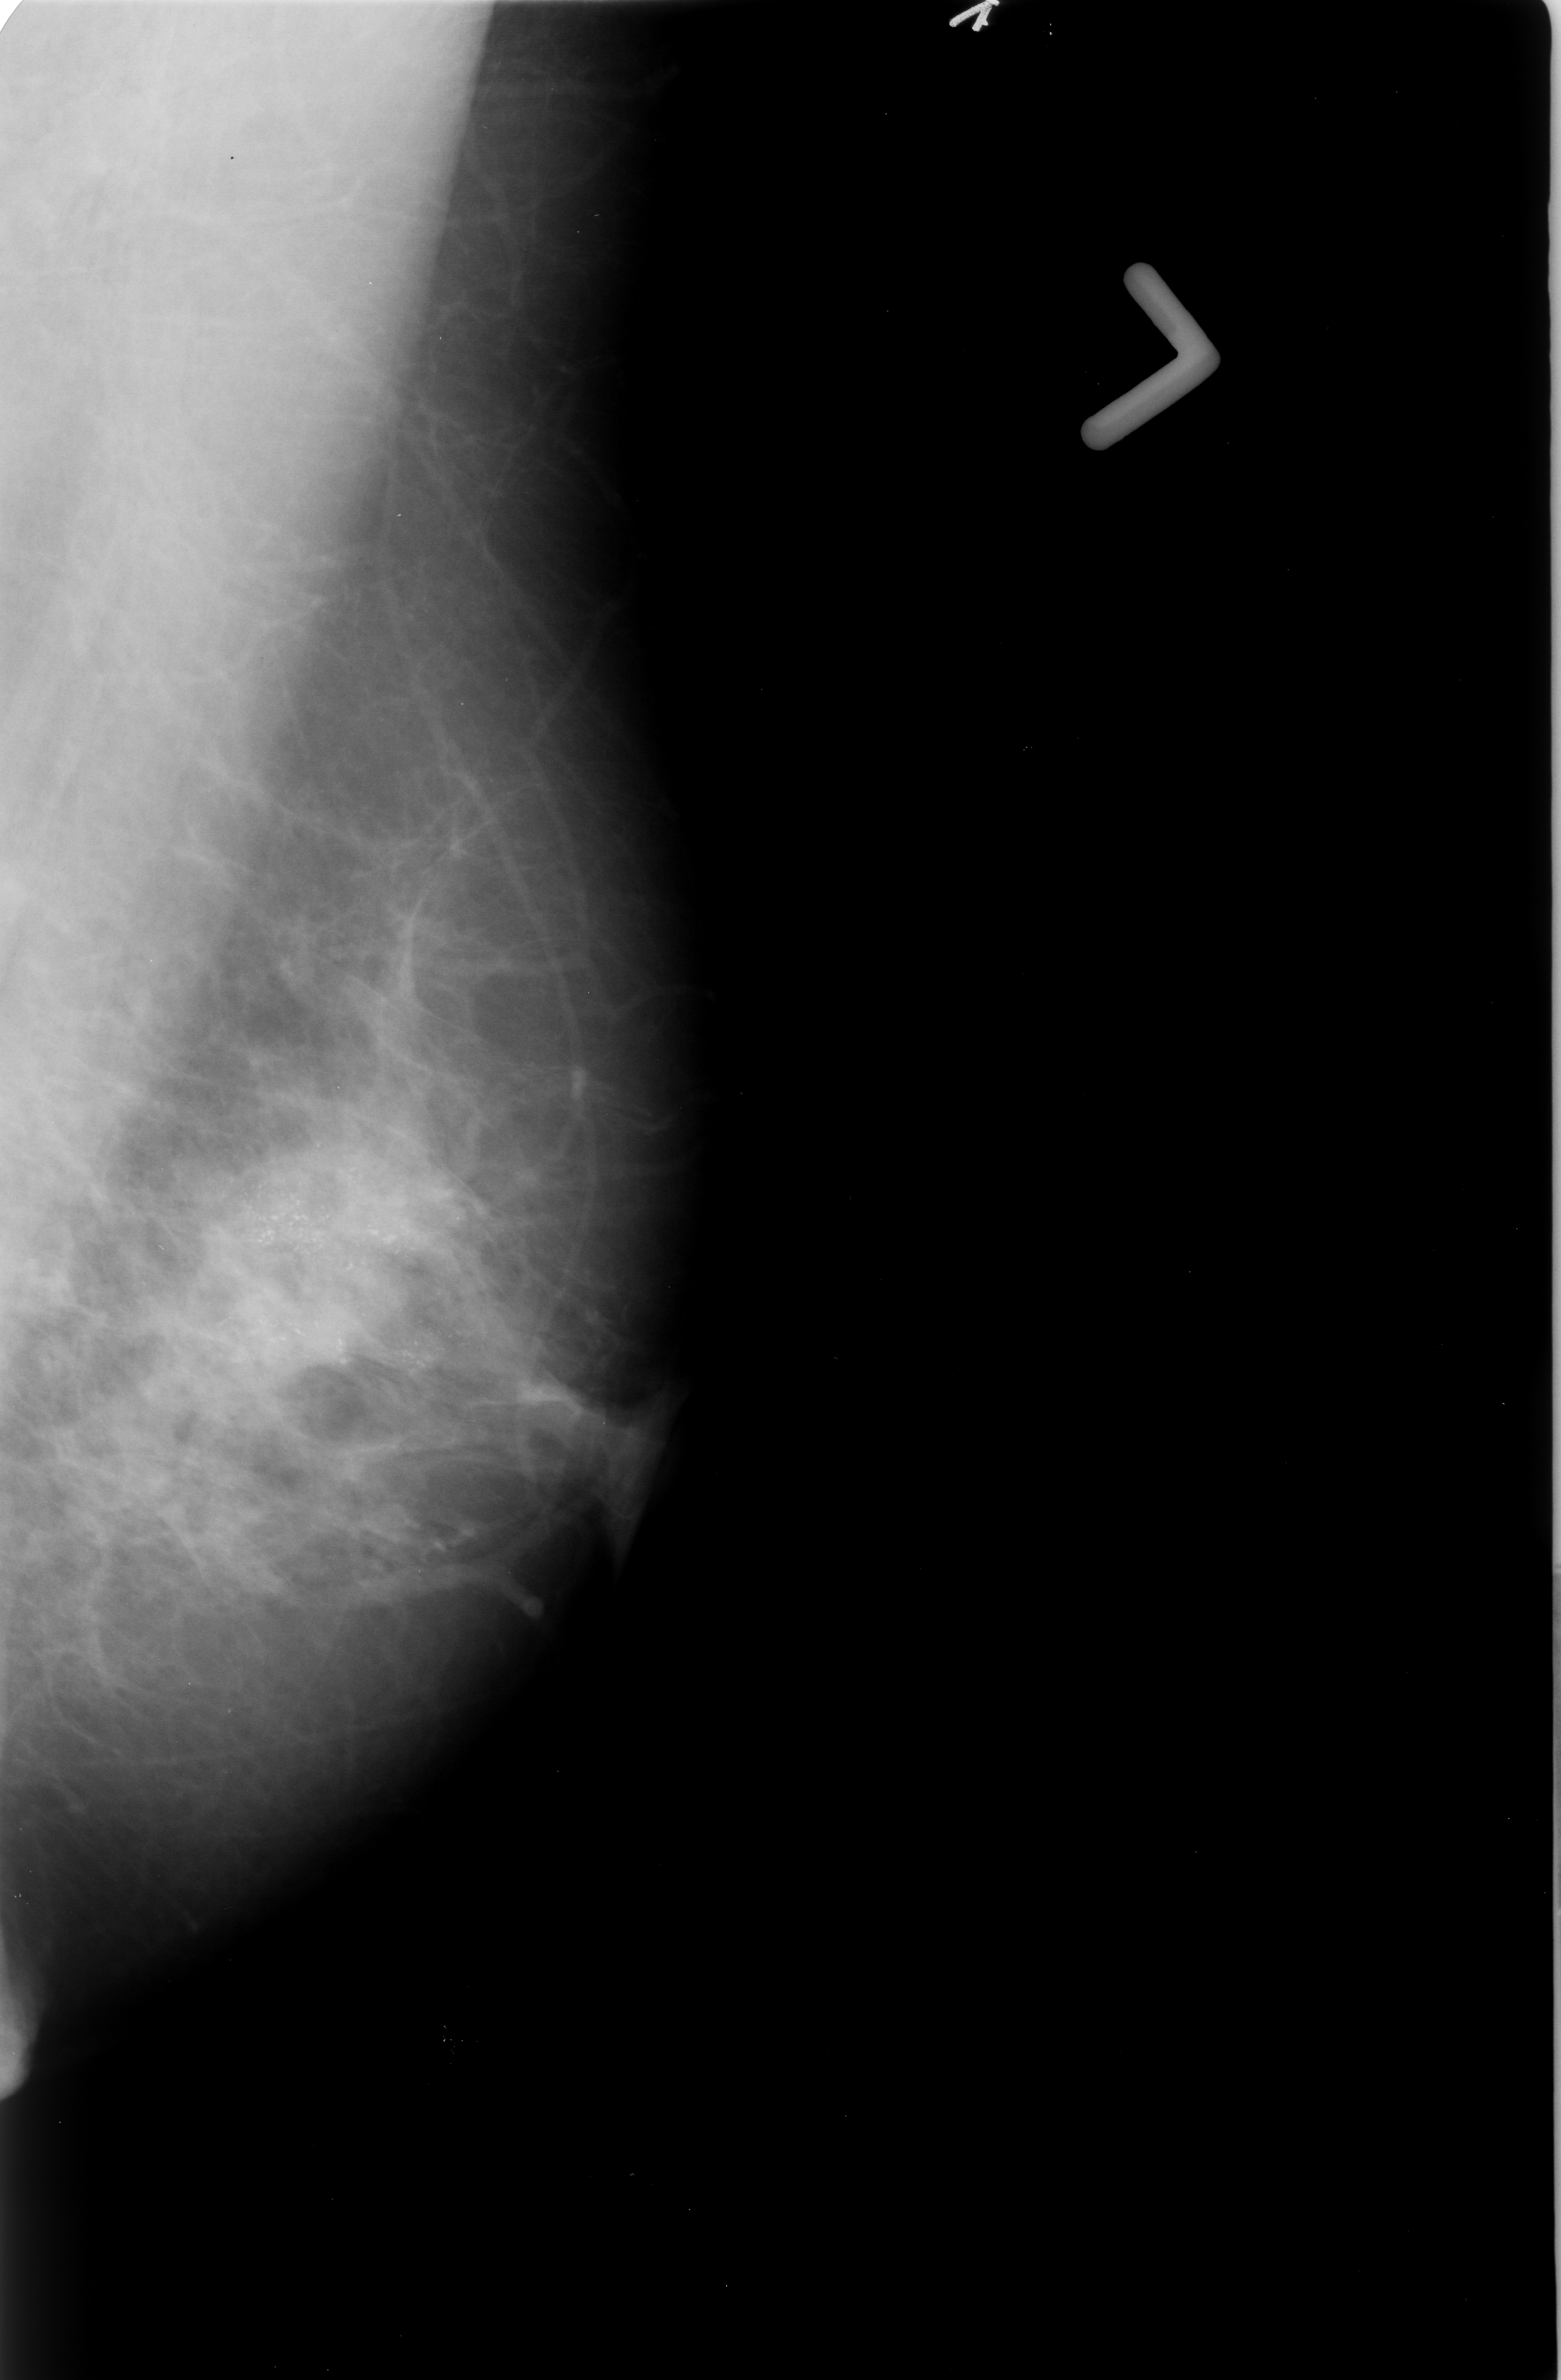
Scanned film-screen mammogram; left breast; mediolateral oblique (MLO) view; breast composition: scattered fibroglandular densities (BI-RADS density category 2 of 4); 1561 × 2380 image matrix.
Marked abnormalities (boxes around the expert regions of interest):
- calcifications, morphology pleomorphic, distribution segmental; BI-RADS assessment category 5; subtlety rating 5 on a 1 (subtle) to 5 (obvious) scale; pathology result (as recorded, not read from the image): malignant: bounding box <146,1061,500,1420> (left, top, right, bottom; pixels)